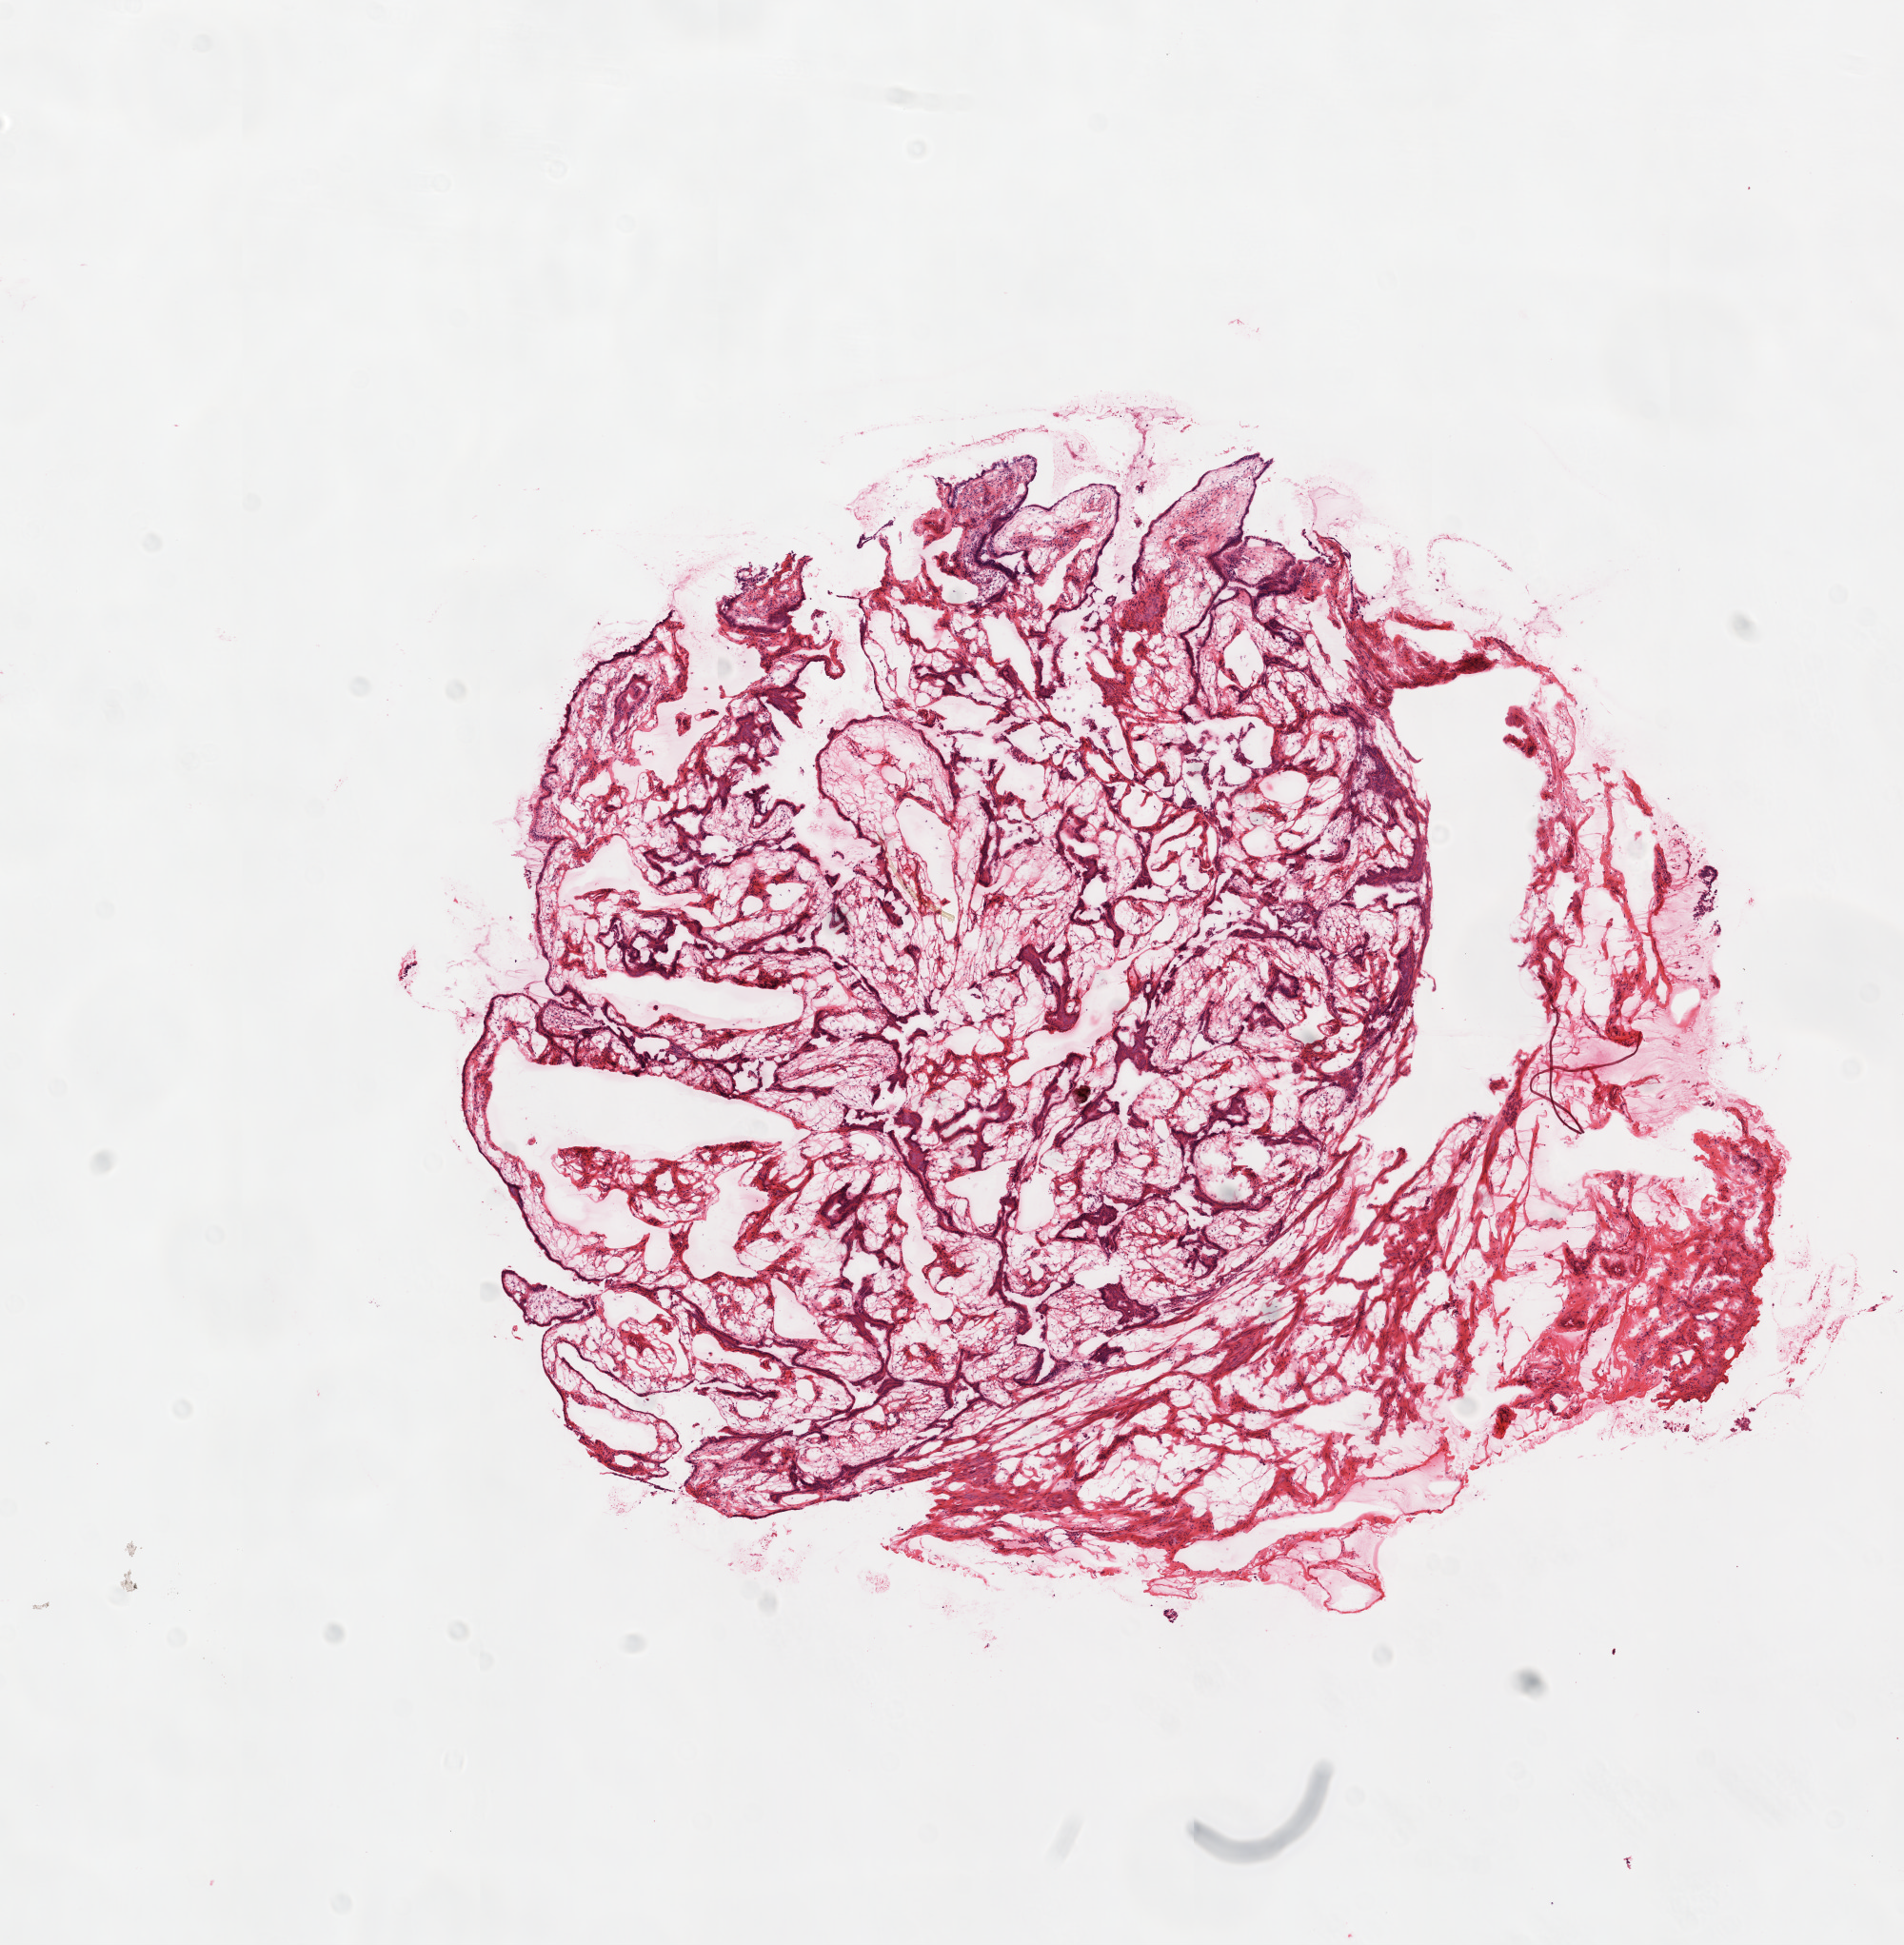
Whole-slide histology image, Hematoxylin and eosin (H&E) stained, a low-resolution overview of the entire scanned area, about 8.0 x 8.2 mm; frozen section from the top of the tissue portion; ovary, solid tissue normal (non-tumour tissue) sample. Female patient; age at initial diagnosis 45 years.
This section: solid tissue normal (non-tumour) sample from the same patient. Patient diagnosis: Serous cystadenocarcinoma, NOS.